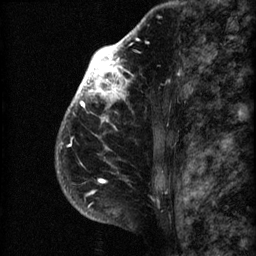
Breast MRI (dynamic contrast-enhanced), one sagittal slice; position 48 of 60 along the scan axis; 3 images stored at this slice position (order not interpretable as contrast timing); 1.5 T; TE 4.2 ms, TR 22.7 ms; 2 mm slice thickness; 256 × 256 image matrix, field of view 180 × 180 mm. Patient: female, 48 years. From the clinical record (not read from this slice): setting: breast cancer imaged before/during neoadjuvant chemotherapy; receptor status: triple-negative.
Structures marked on this image (semi-automatically segmented with operator editing):
- analysis volume of interest (the breast-tissue region the enhancement analysis was run in; not a lesion): bounding box [x1, y1, x2, y2] px = [55, 30, 173, 207]
- tumour enhancement mask (voxels above the 90 % enhancement threshold inside the analysis volume of interest): [57, 31, 137, 207]